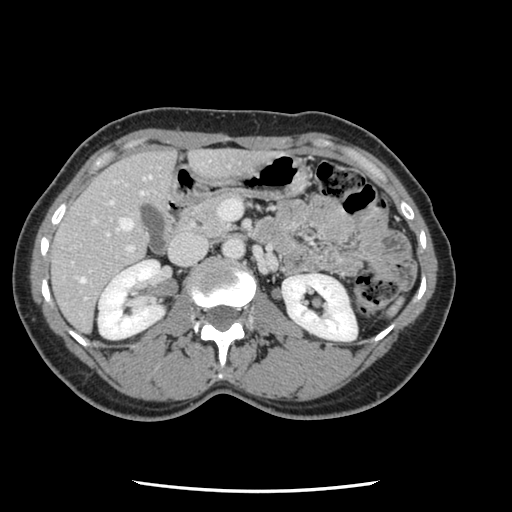
Contrast-enhanced abdominal CT, one axial slice. Position 50 of 134 along the scan axis. 120 kVp. Intravenous contrast given. Soft-tissue window (W 400 / L 40 HU). 2.5 mm slice thickness. 512 × 512 image matrix. Female patient, age 43 years. Case-level facts recorded for this patient, not image findings: diagnosis: colorectal cancer liver metastases, imaged before liver resection; multiple liver metastases: yes; largest metastasis: 3.4 cm; disease in both lobes: yes.
Structures marked on this image (expert manual segmentation):
- hepatic veins: box from (x=79, y=176) to (x=152, y=284) px
- liver: (x=52, y=150)–(x=261, y=331)
- planned liver remnant (the part of the liver to remain after resection): (x=51, y=150)–(x=175, y=330)
- portal vein (with intrahepatic branches): (x=71, y=201)–(x=242, y=301)